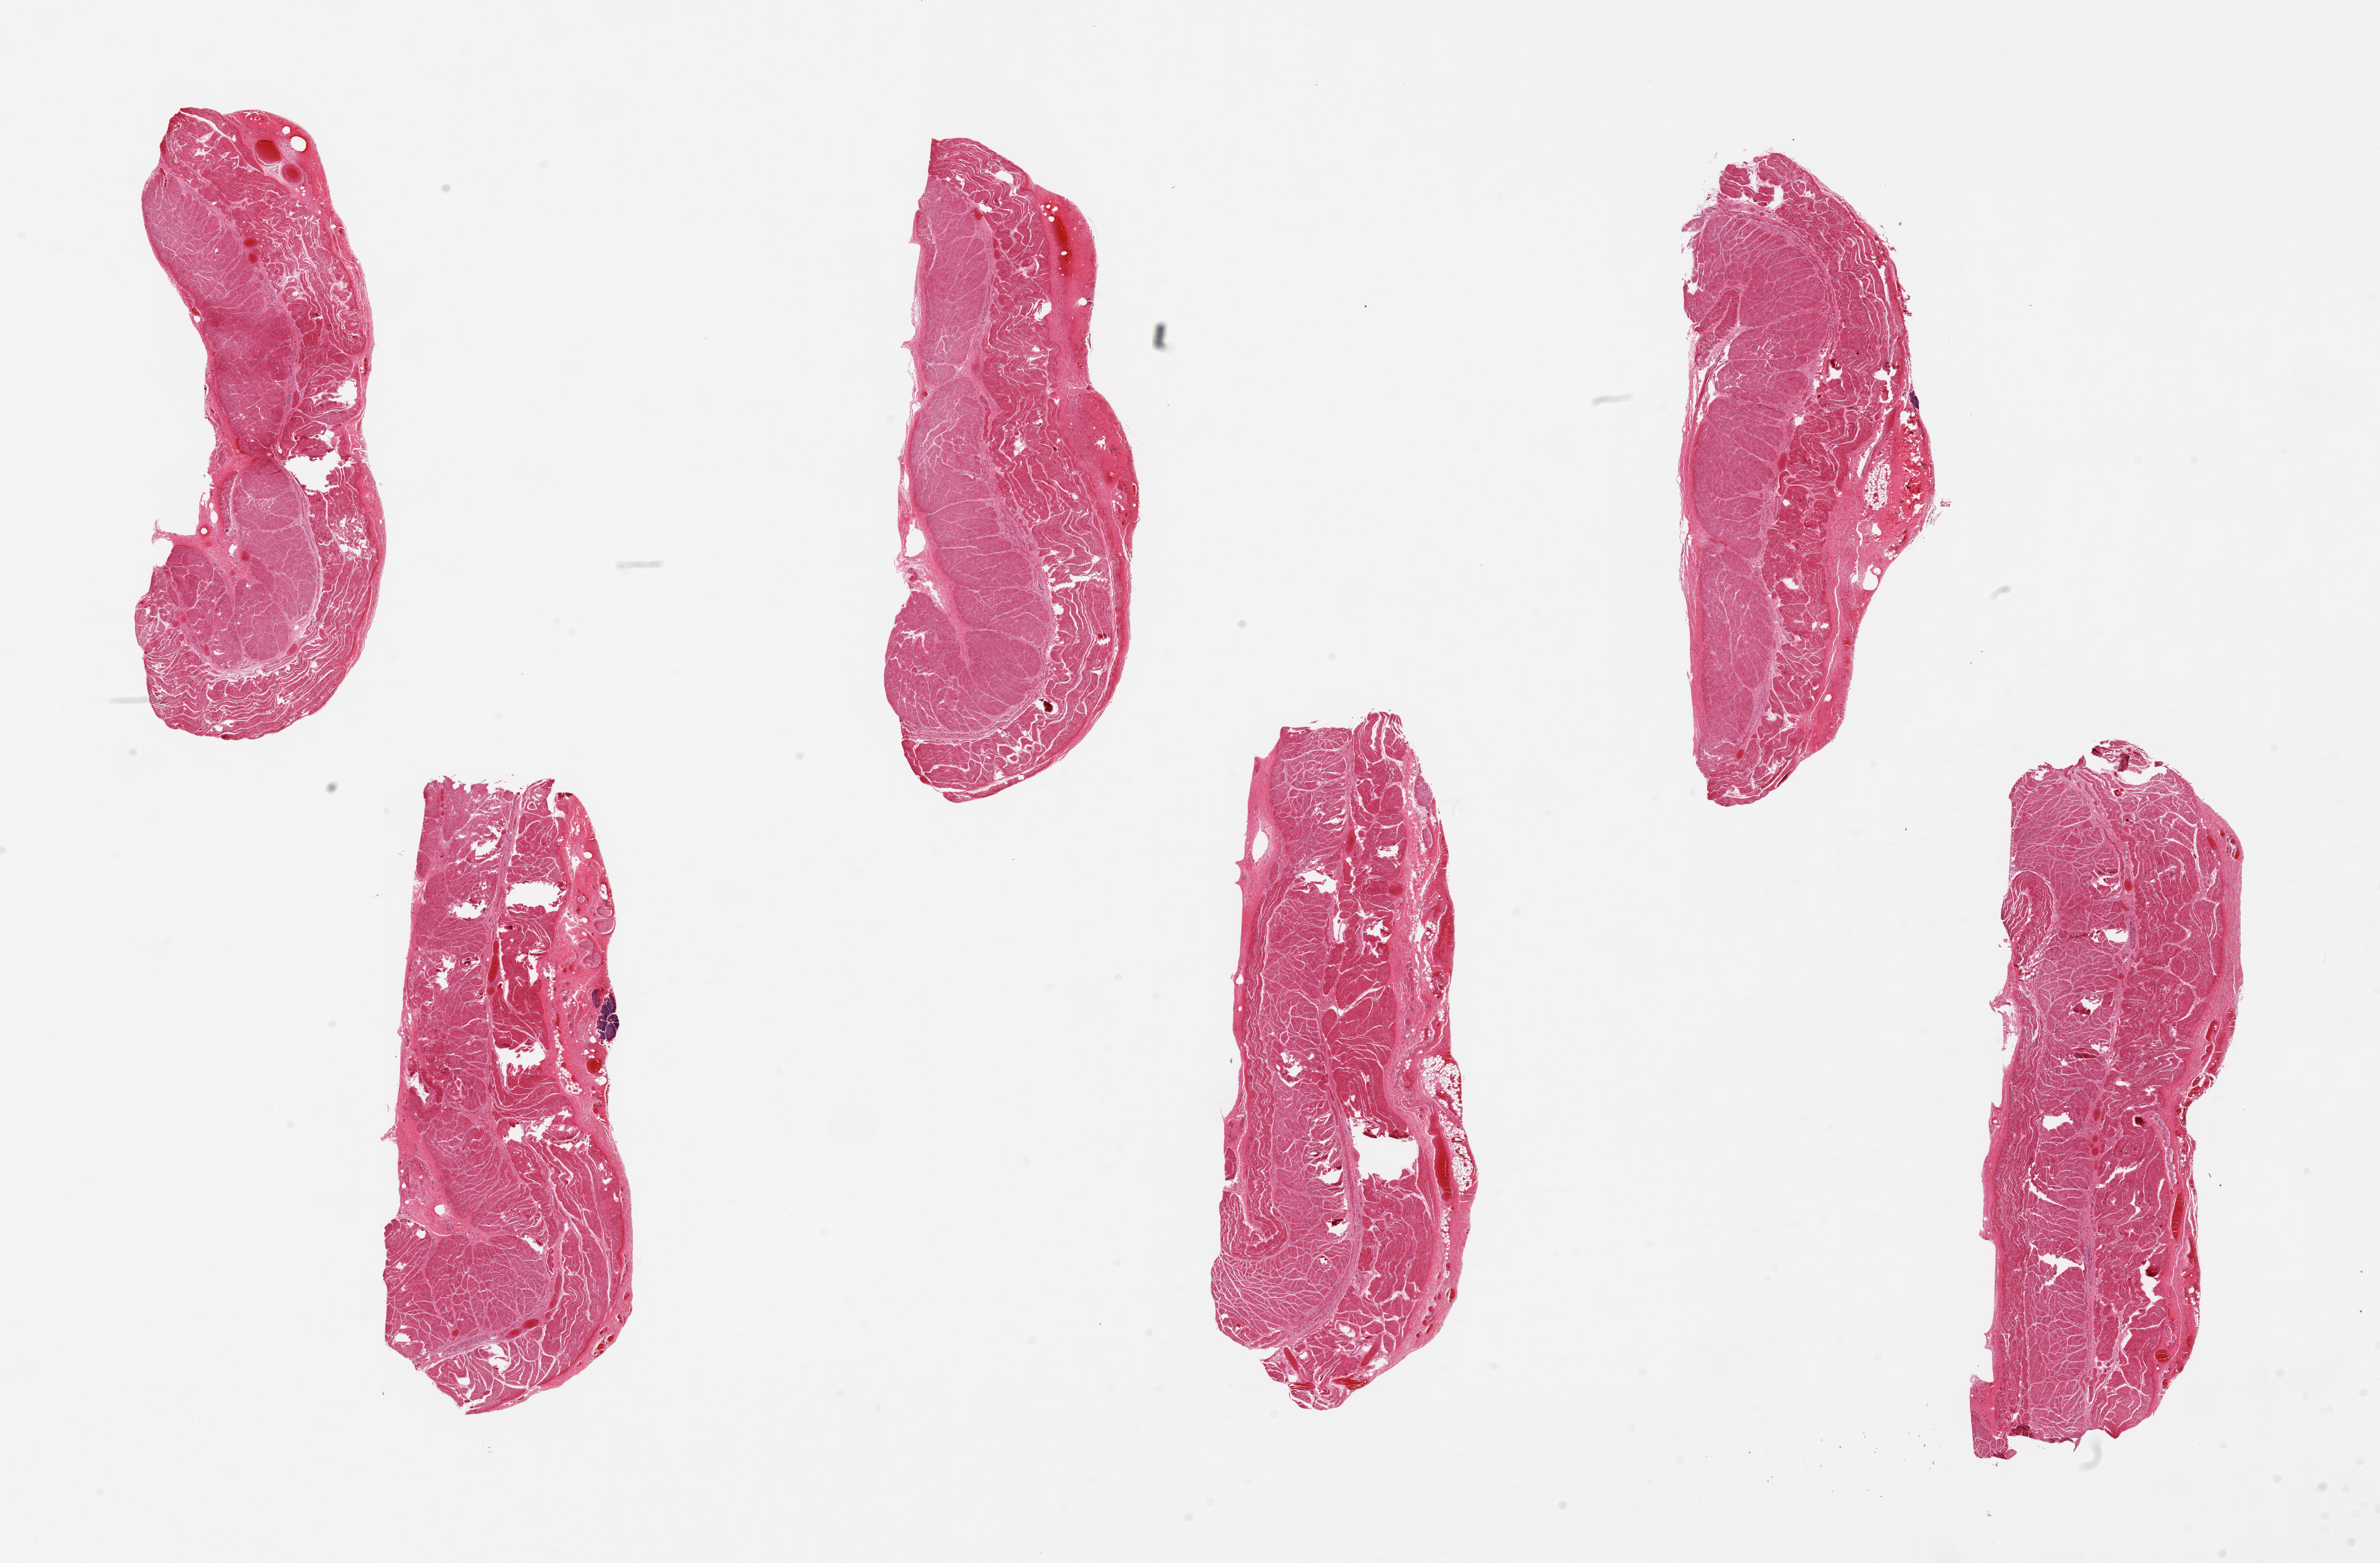
Digitized H&E-stained section, brightfield, a low-resolution overview of the entire scanned area, about 30.5 x 20.0 mm (acquisition: 20x scan), PAXgene-fixed paraffin-embedded (PFPE) section, target tissue: esophageal muscle, tissue donor sample. Donor: male.
- pathologist's review note for this sample: 6 pieces, up to 9x3mm; all muscularis, good specimens